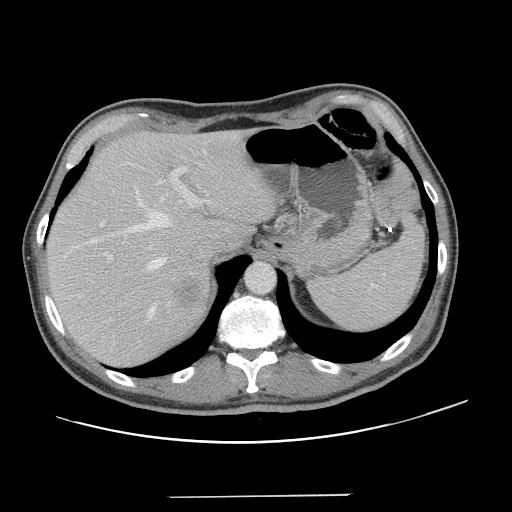
Contrast-enhanced abdominal CT, one axial slice; position 99 of 131 along the scan axis; intravenous contrast given; soft-tissue window (W 400 / L 40 HU); 512 × 512 image matrix. Male patient, age 60 years. From the clinical record (not read from this slice): diagnosis: colorectal cancer liver metastases, imaged before liver resection; multiple liver metastases: no; largest metastasis: 2.5 cm.
Annotated regions visible in this slice (manually delineated by an expert):
- hepatic veins: bounding box <91,188,174,319> (left, top, right, bottom; pixels)
- liver: <47,131,274,366>
- planned liver remnant (the part of the liver to remain after resection): <47,131,275,352>
- portal vein (with intrahepatic branches): <99,149,213,262>
- liver metastasis: <175,278,202,308>